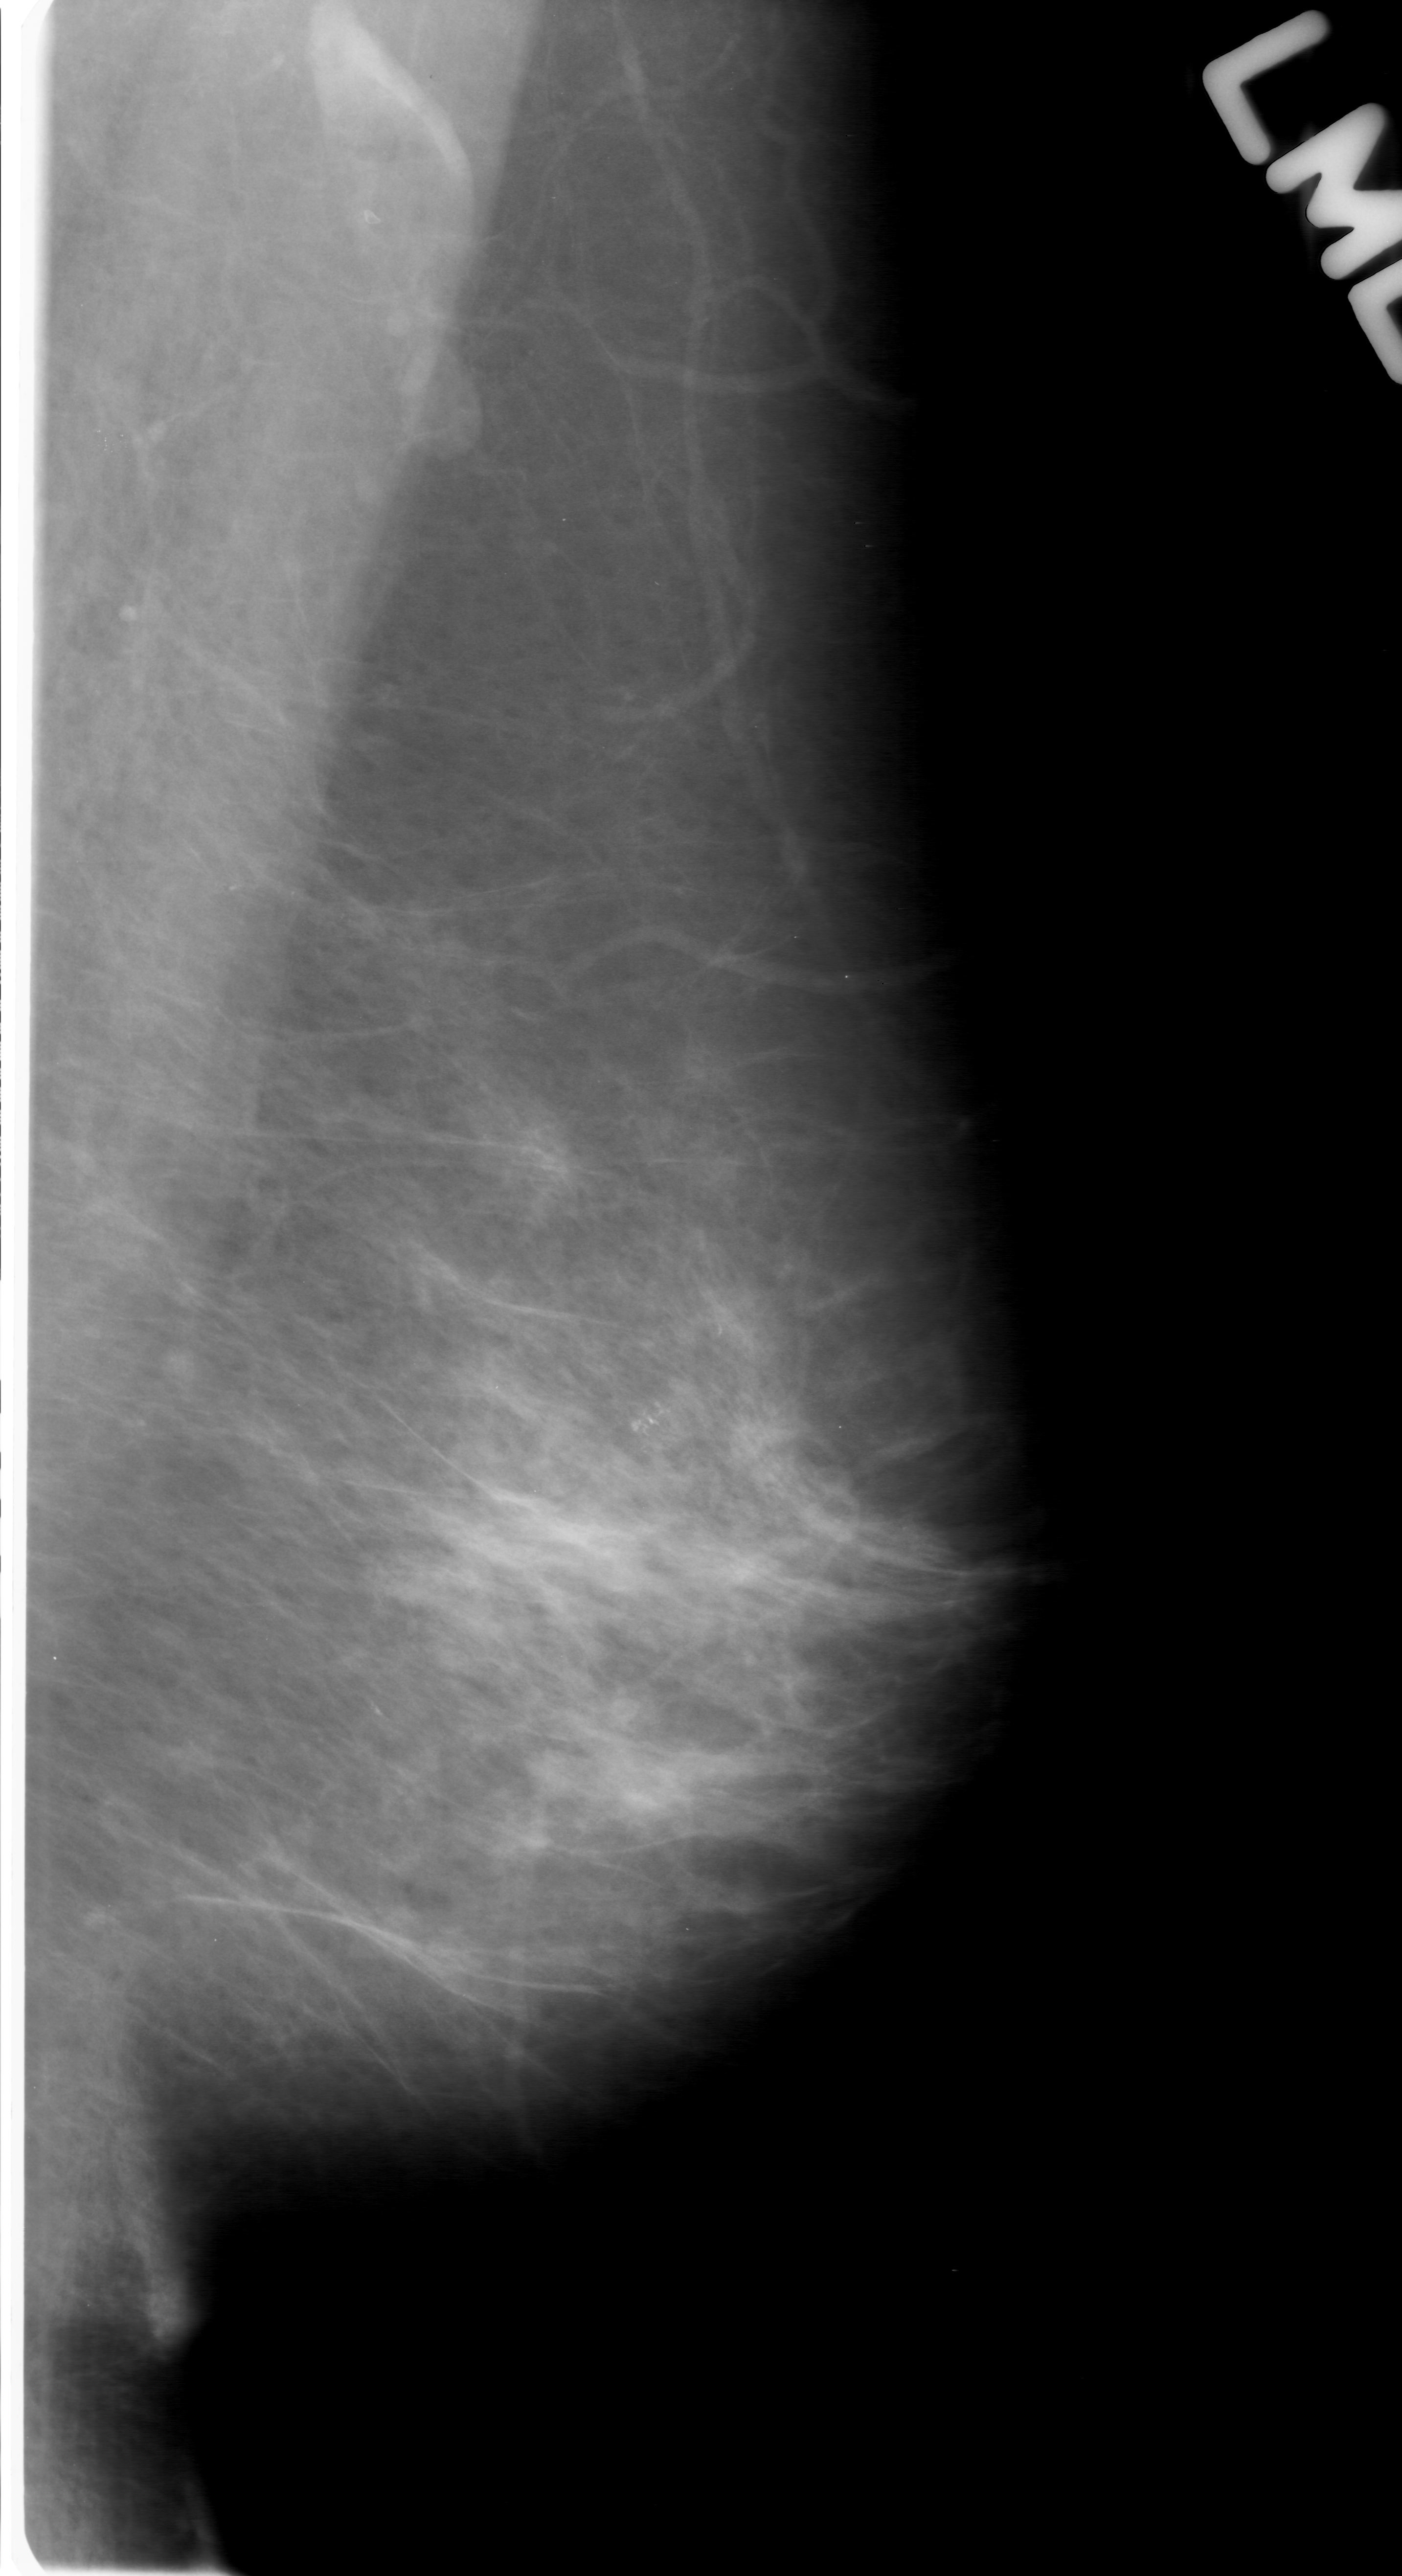
Digitized screen-film mammogram. Left breast. Mediolateral oblique (MLO) view. 1402 × 2576 image matrix.
Expert-marked regions of interest on this image (one box per marked abnormality):
- calcifications, morphology pleomorphic, distribution clustered; BI-RADS assessment category 3; pathology (as recorded): malignant: bounding box <480,1262,792,1586> (left, top, right, bottom; pixels)